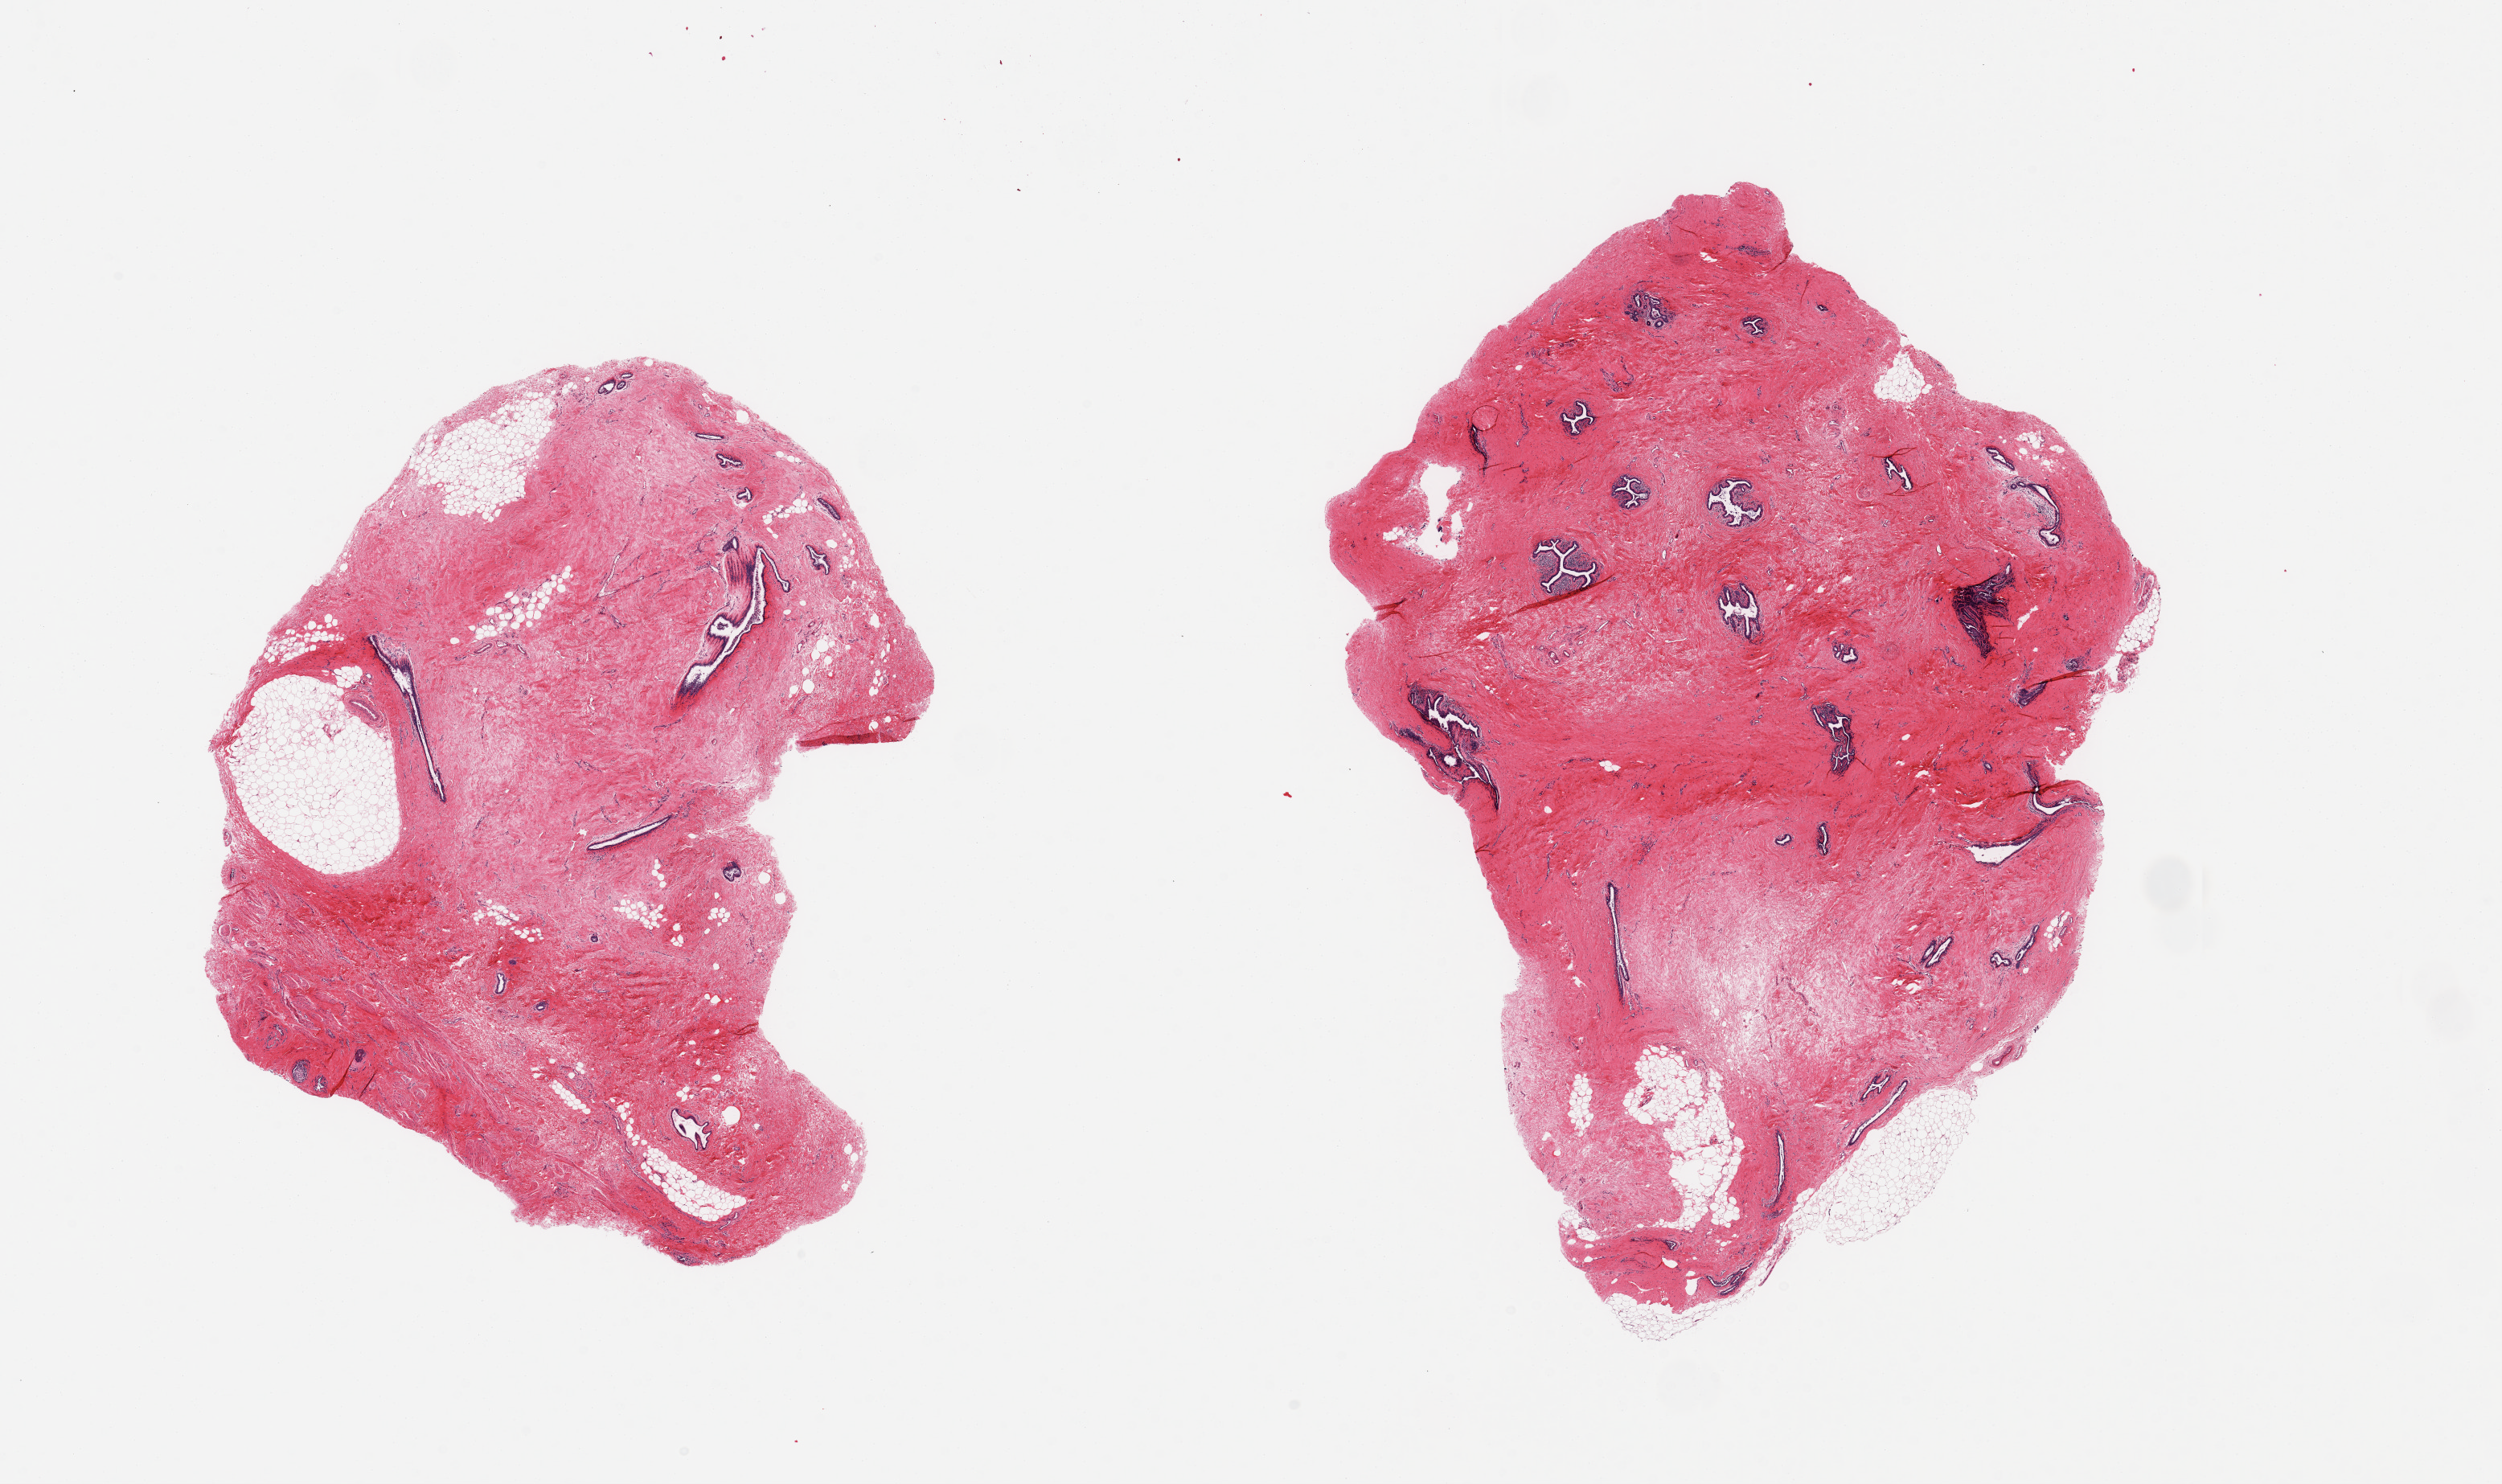
Digitized haematoxylin and eosin-stained section — low-resolution overview of the scanned area, about 24.6 x 14.6 mm (from a 20x scan); PAXgene-fixed, paraffin-embedded tissue; target tissue: breast; donor tissue sample.
- review note (as recorded): 2 pieces, prominent gynecomastoid ductal and stromal hyperplasia